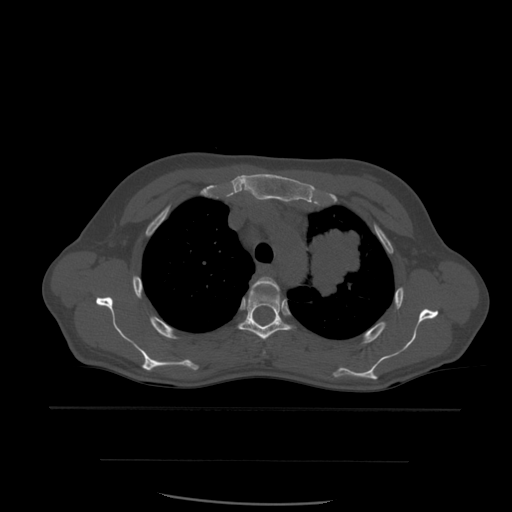
CT including the spine, one axial slice. Slice 429 of 574 in the series (ordered by position). Bone window (W 1800 / L 400 HU). 1.25 mm slice thickness. 512 × 512 image matrix, field of view 392 × 392 mm. Patient age 48 years. Case-level facts recorded for this patient, not image findings: primary cancer: lung; vertebrae with lytic lesions (as recorded): T11.
Outlined on this slice (semi-automatic segmentation, software-assisted and operator-edited):
- T3 vertebra: box from (x=250, y=277) to (x=281, y=301) px
- T4 vertebra: (x=238, y=292)–(x=292, y=341)